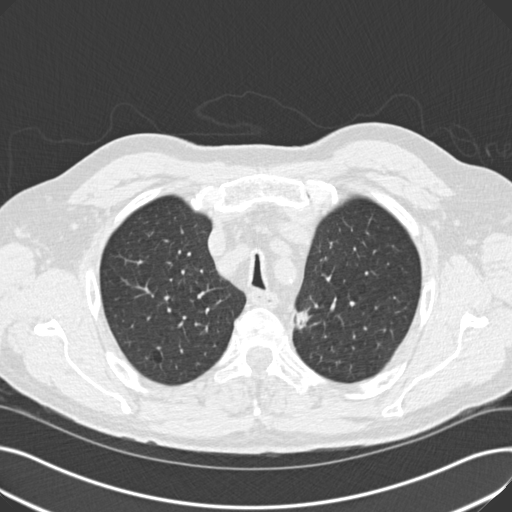
Chest CT (low-dose screening protocol), one axial image; second screening round (one year after baseline); lung window (W 1500 / L -600 HU); standard (soft-tissue) reconstruction kernel (B30f); 140 kVp; 512 × 512 image matrix. Male participant, aged 70 years at enrolment. Current smoker at enrolment.
• Expert-annotated lung lesion, bounding box (x1, y1, x2, y2) in pixels: (280, 297, 321, 340).
• The screening reader recorded 2 non-calcified nodules or masses ≥4 mm on this exam; which of them this box marks is not recorded.
• Participant outcome: lung cancer diagnosed 581 days after this screen (after the third annual screen) — mixed cell adenocarcinoma, left upper lobe, poorly differentiated (G3), stage IIB (AJCC 6th edition), 17 mm at pathology.